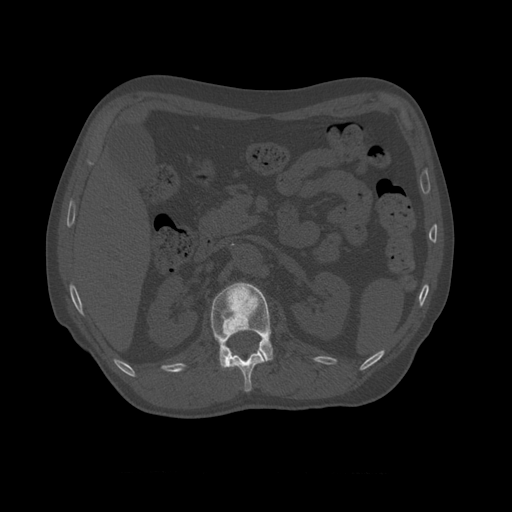
CT including the spine, one axial slice. Position 364 of 450 along the scan axis. Reconstruction kernel STANDARD. Bone window (W 1800 / L 400 HU). 1.25 mm slice thickness. 512 × 512 image matrix, field of view 405 × 405 mm. Patient age 75 years. From the clinical record (not read from this slice): primary cancer: prostate.
Outlined on this slice (semi-automatically segmented with operator editing):
- L1 vertebra: bounding box <211,282,274,371> (left, top, right, bottom; pixels)
- T10 vertebra: <223,345,273,369>
- T11 vertebra: <225,350,265,393>